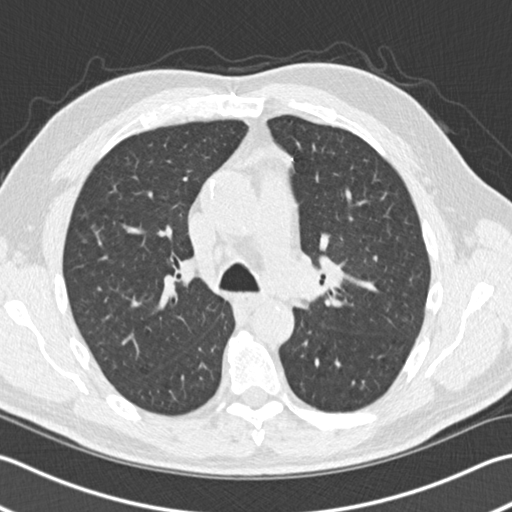
Low-dose screening chest CT, one axial slice. 120 kVp. Lung window (W 1500 / L -600 HU). 2 mm slice thickness. 512 × 512 image matrix, field of view 346 × 346 mm.
Structures marked on this image (manually delineated by an expert):
- lesion 1 (tumor, upper lobe of left lung): bounding box (x1, y1, x2, y2) in pixels: (325, 272, 342, 289)